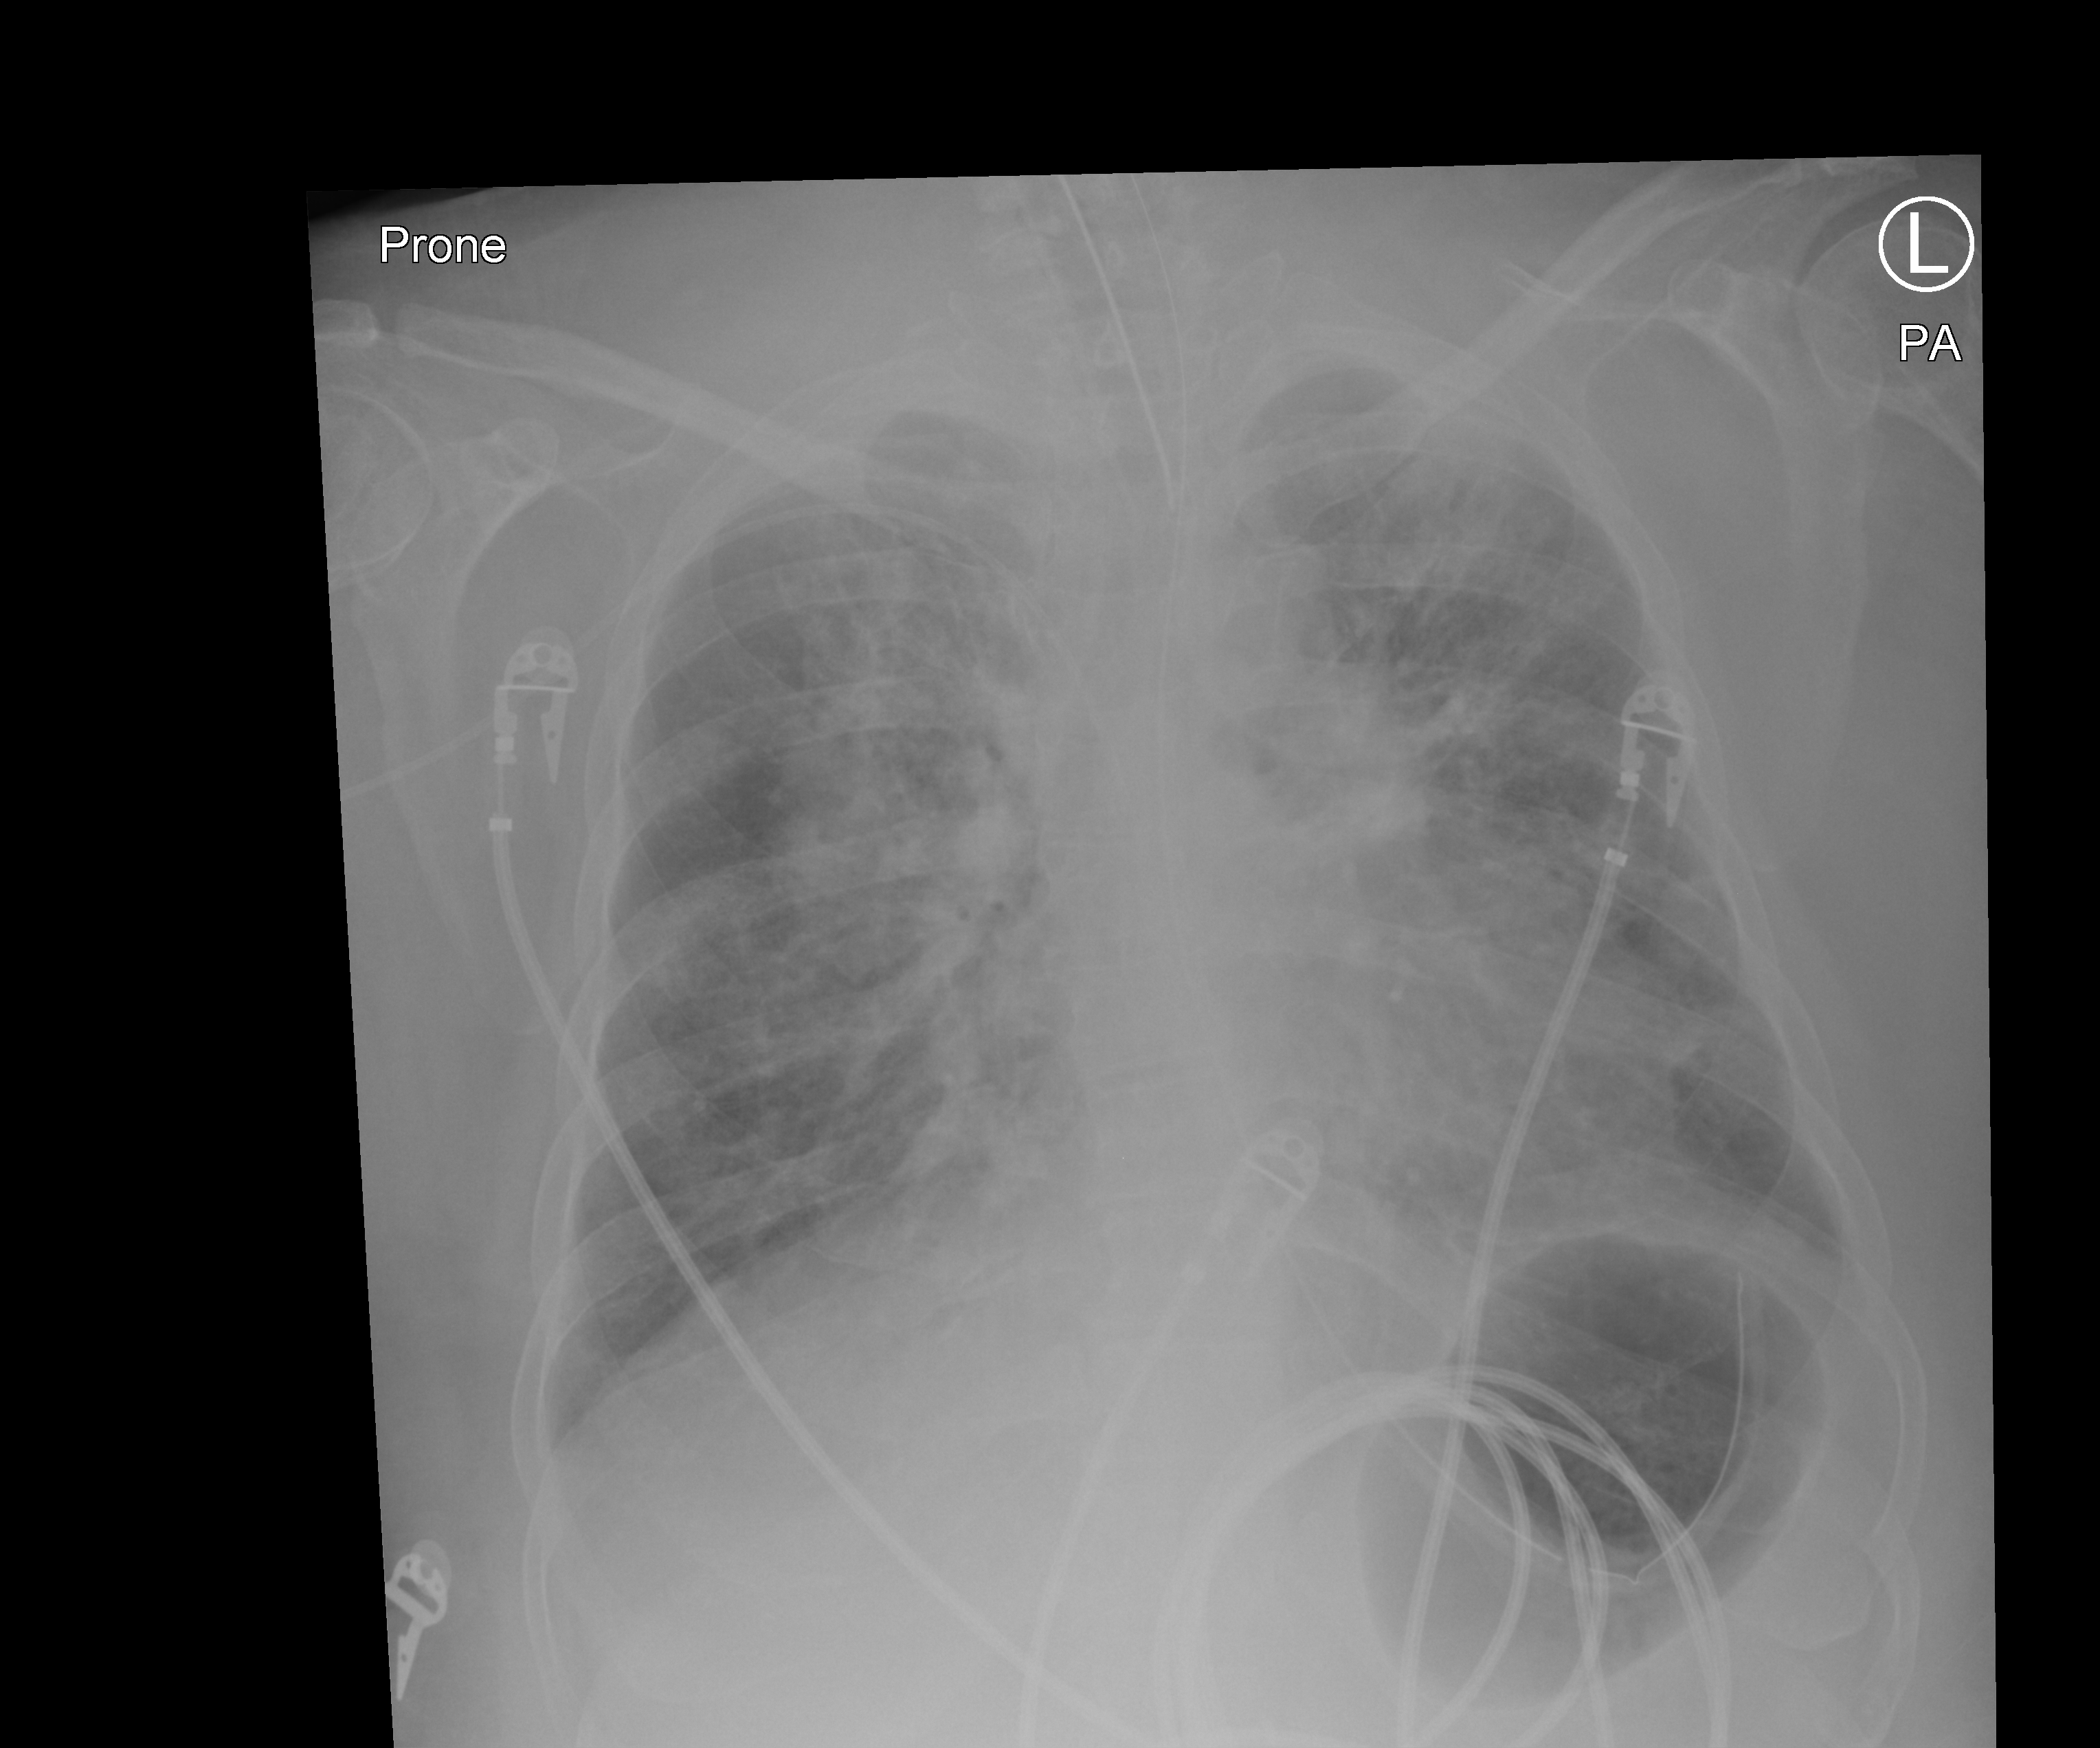
Bedside chest radiograph (computed radiography), posteroanterior (PA) projection. Patient hospitalised with COVID-19, aged 18–59 years.
From the hospital-stay record, not from the radiograph (when in the stay this image was taken is not recorded):
- admitted to intensive care during this hospital stay: yes